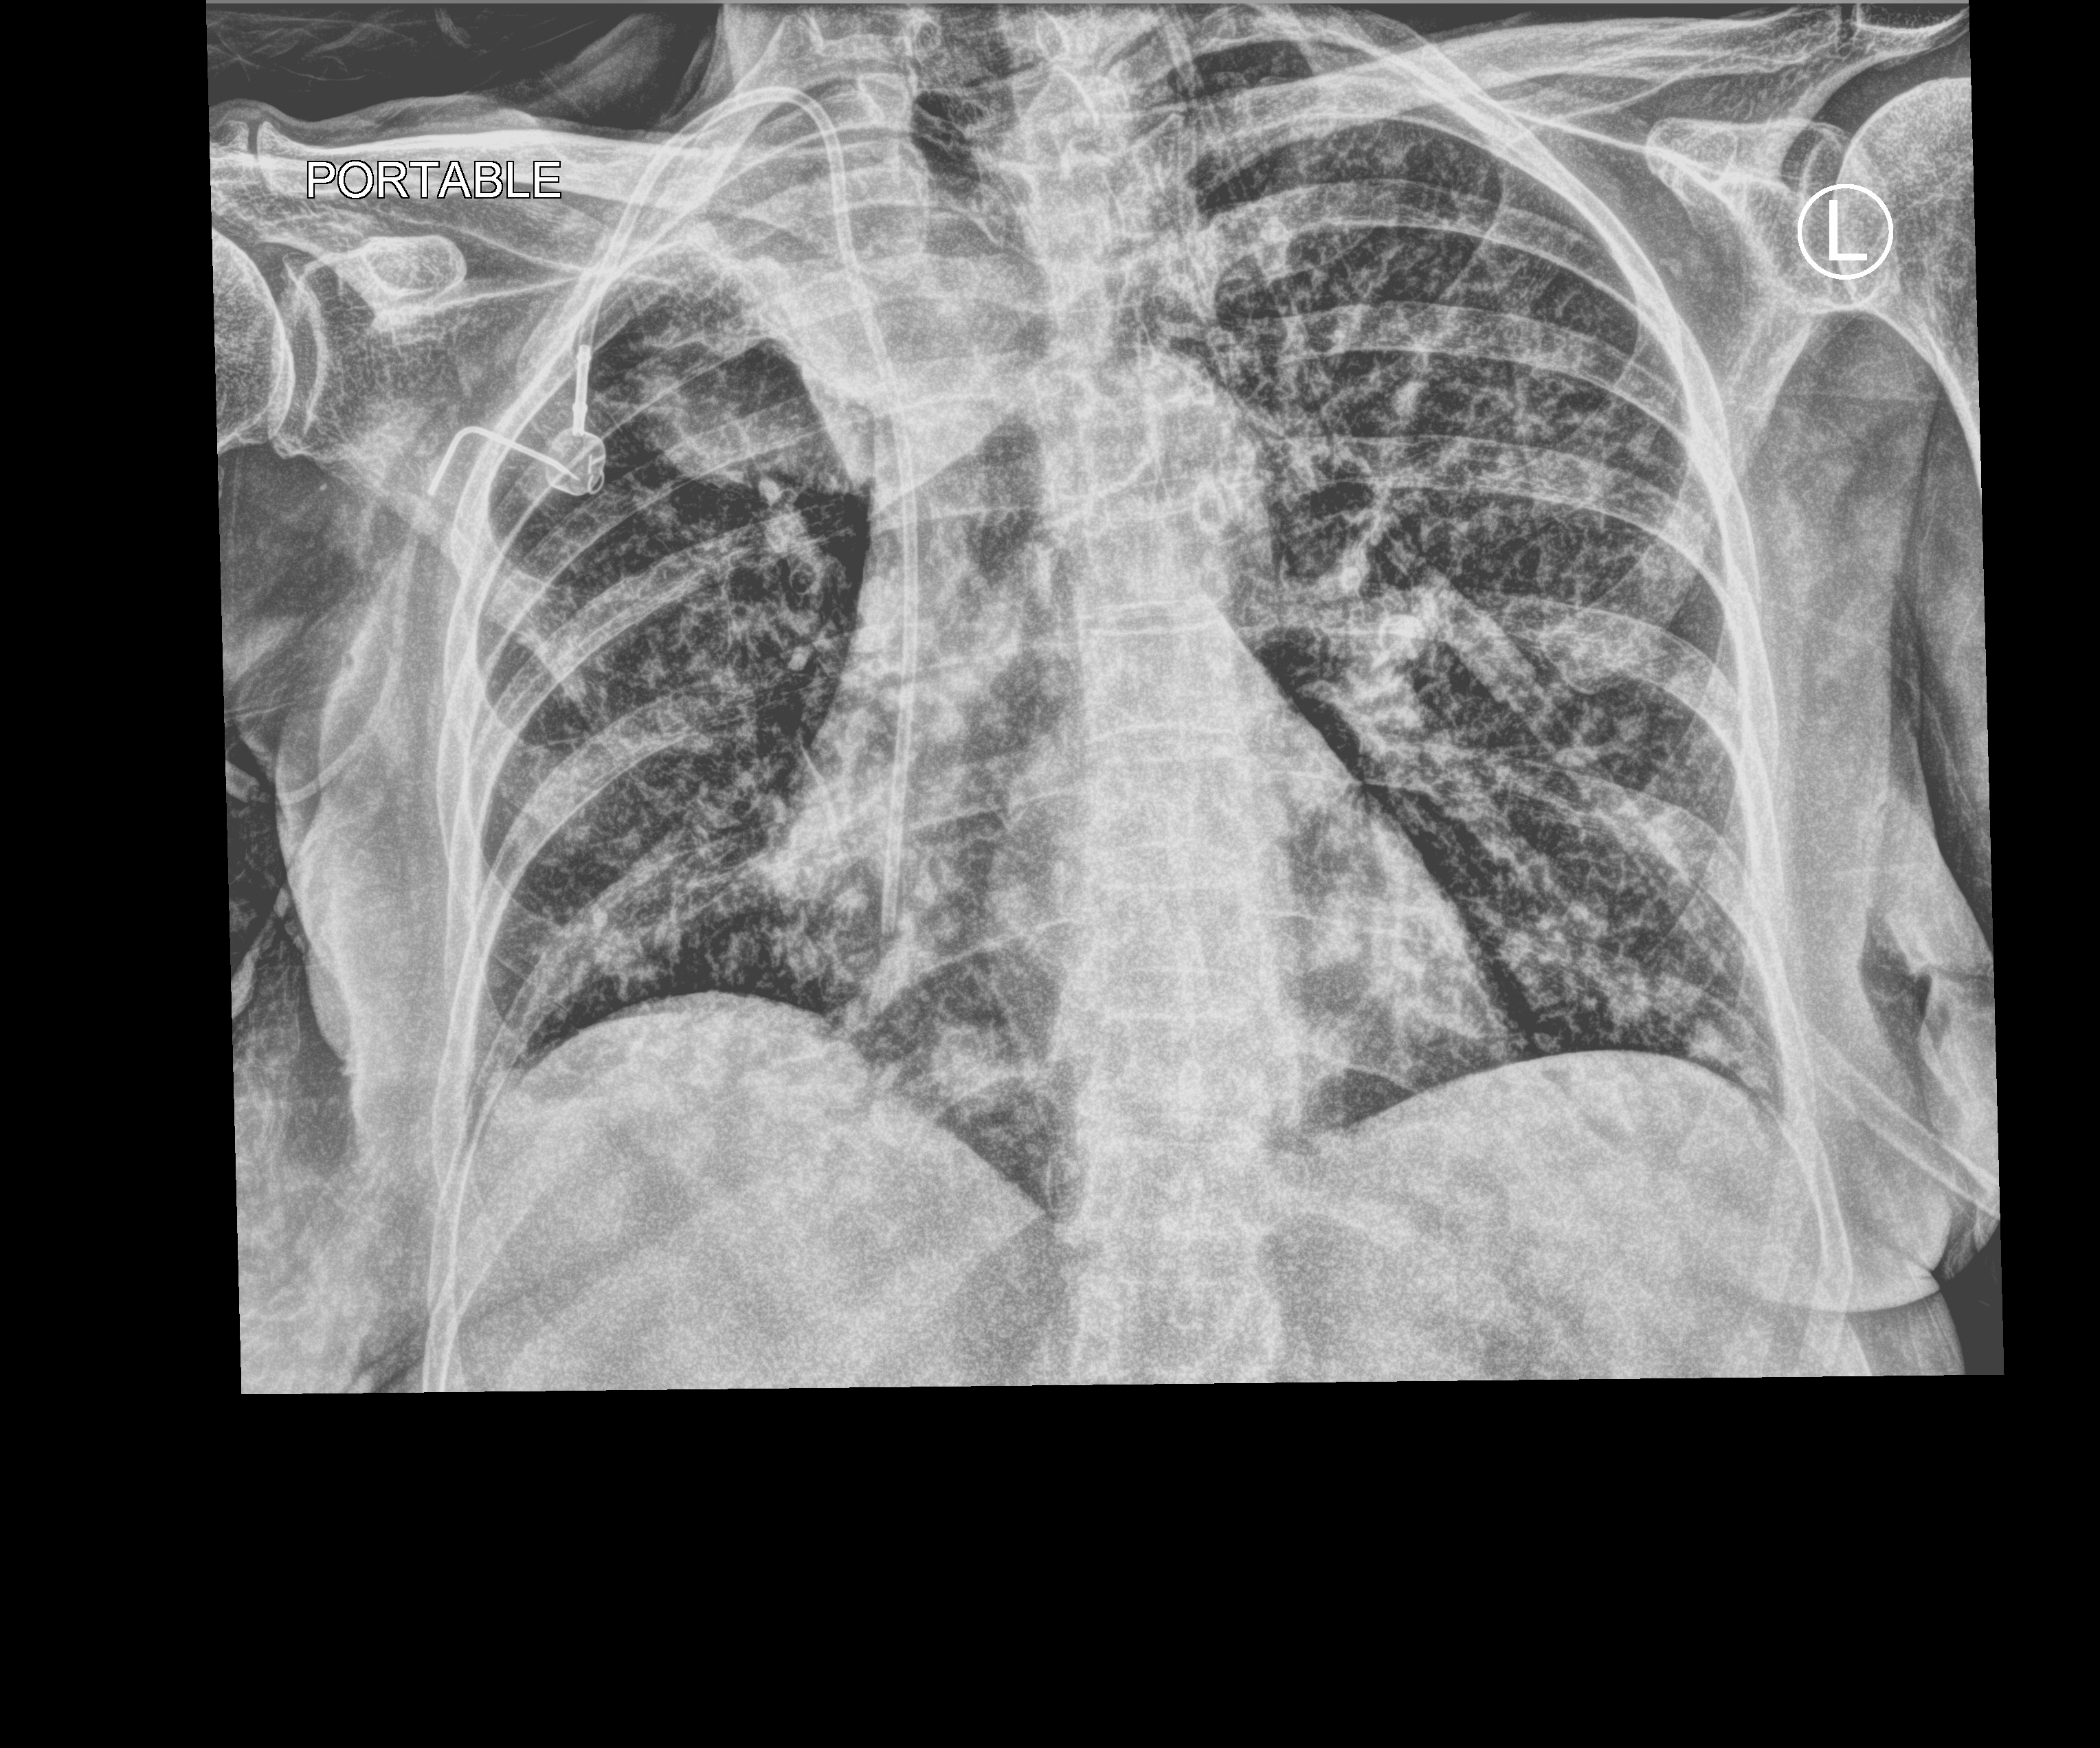
Portable chest radiograph; anteroposterior (AP) projection. Female patient hospitalised with COVID-19, age 60–74 years.
Admission-level facts for this patient (not findings on this image; timing relative to this image not recorded): mechanically ventilated during this hospital stay: no.